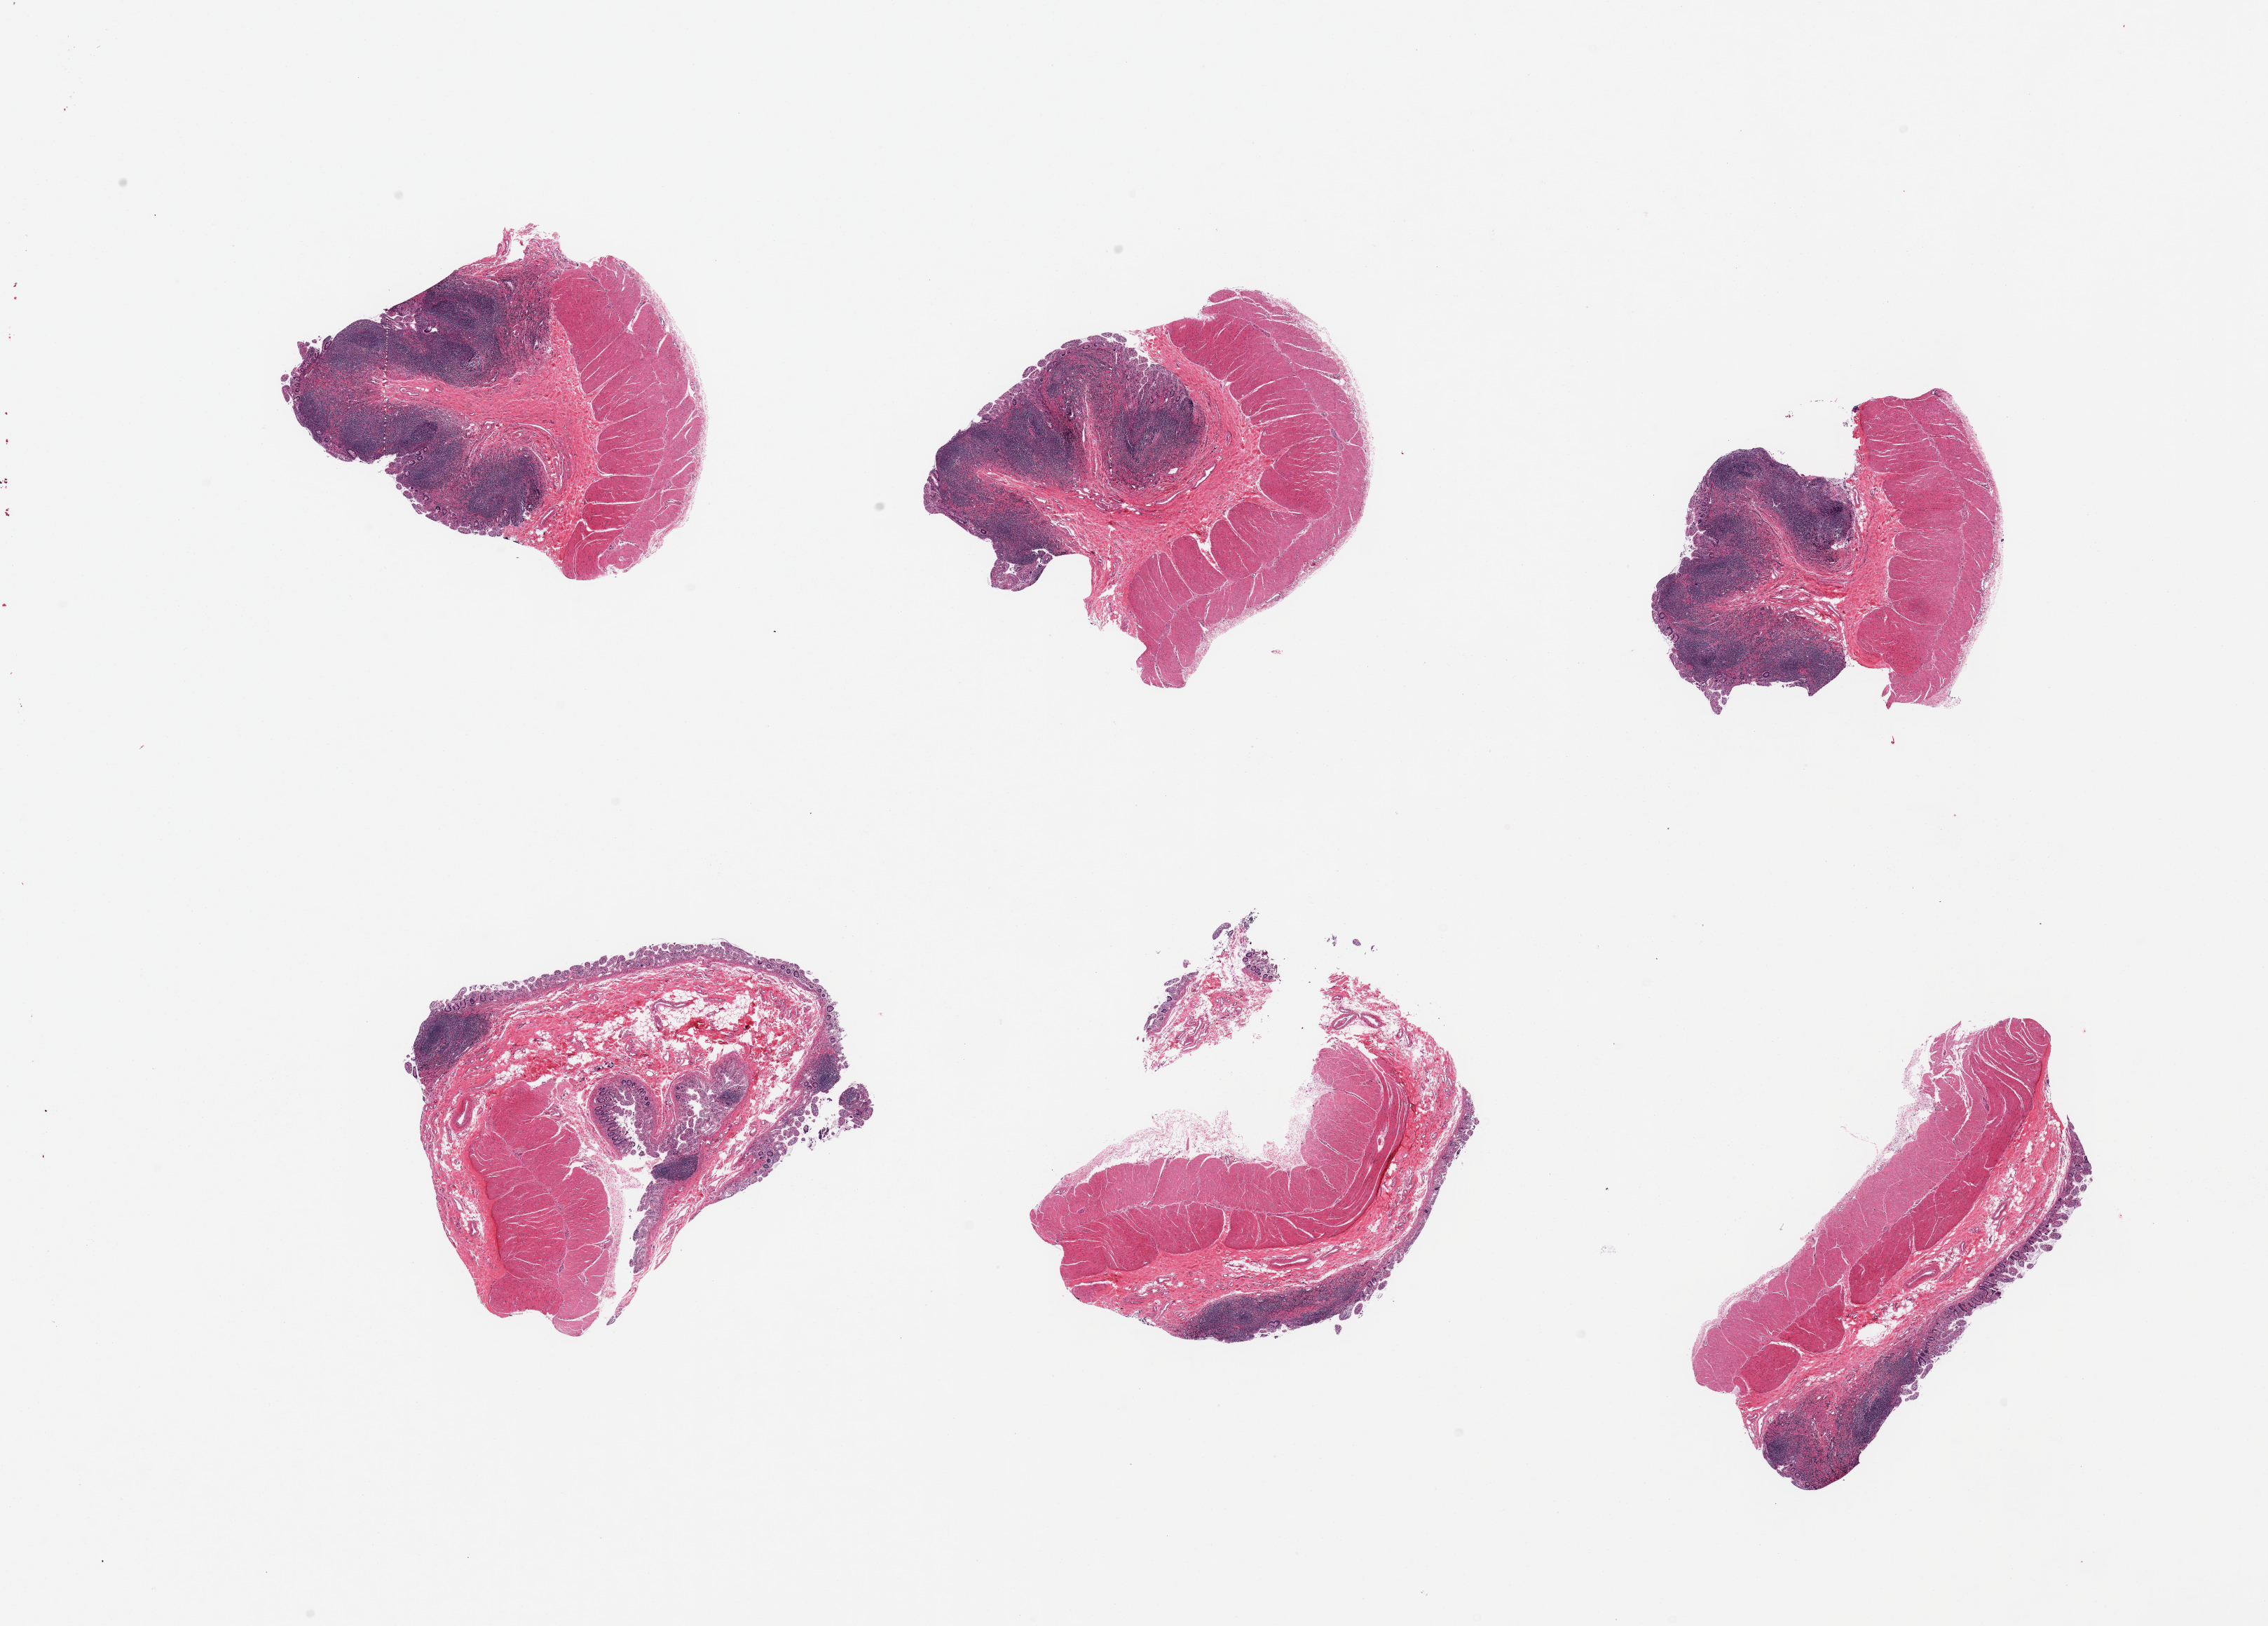
Digitized H&E-stained section — shown as a low-resolution overview of the whole scanned area (about 25.6 x 18.4 mm, slide scanned at 20x); PAXgene-fixed, paraffin-embedded tissue; target tissue: ileum; tissue donor sample.
Reviewer comment on this tissue sample: 6 pieces; moderate to severe autolysis of mucosa and preserved muscularis; abundant residual mucosal lymphoid aggregates.